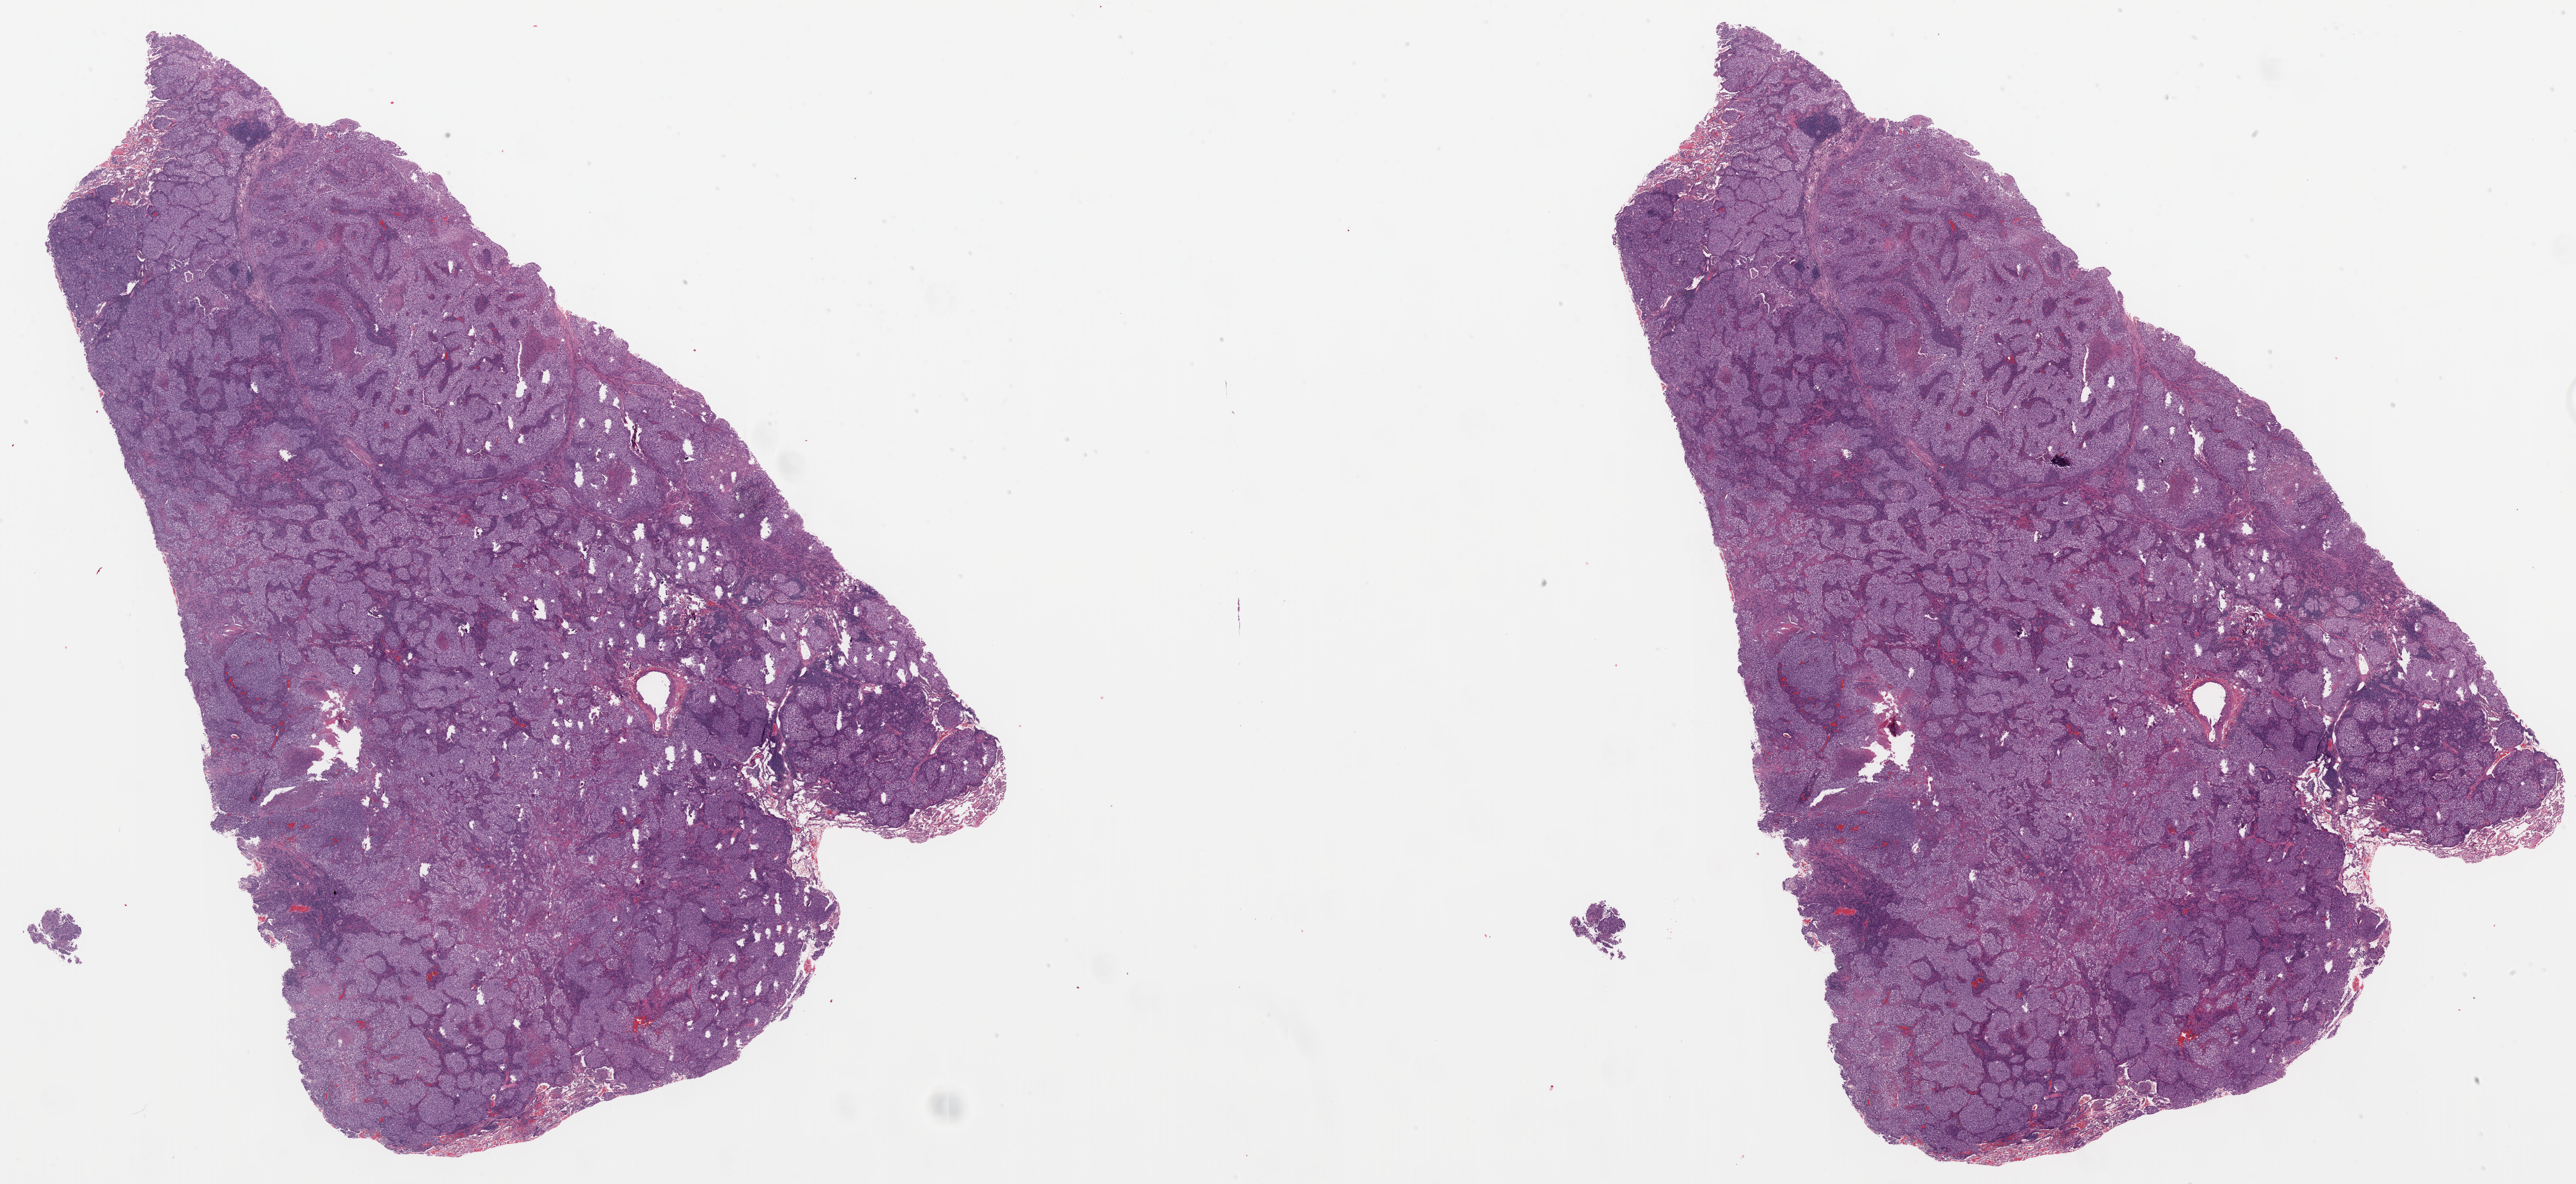
Digitized Hematoxylin and eosin (H&E) stained tissue section (whole slide) — a low-resolution overview of the entire scanned area, about 38.0 x 17.5 mm, formalin-fixed paraffin-embedded (FFPE) diagnostic section, sample: primary tumour, lung. Male patient.
Pathologic diagnosis: Solid carcinoma, NOS (upper lobe, lung).